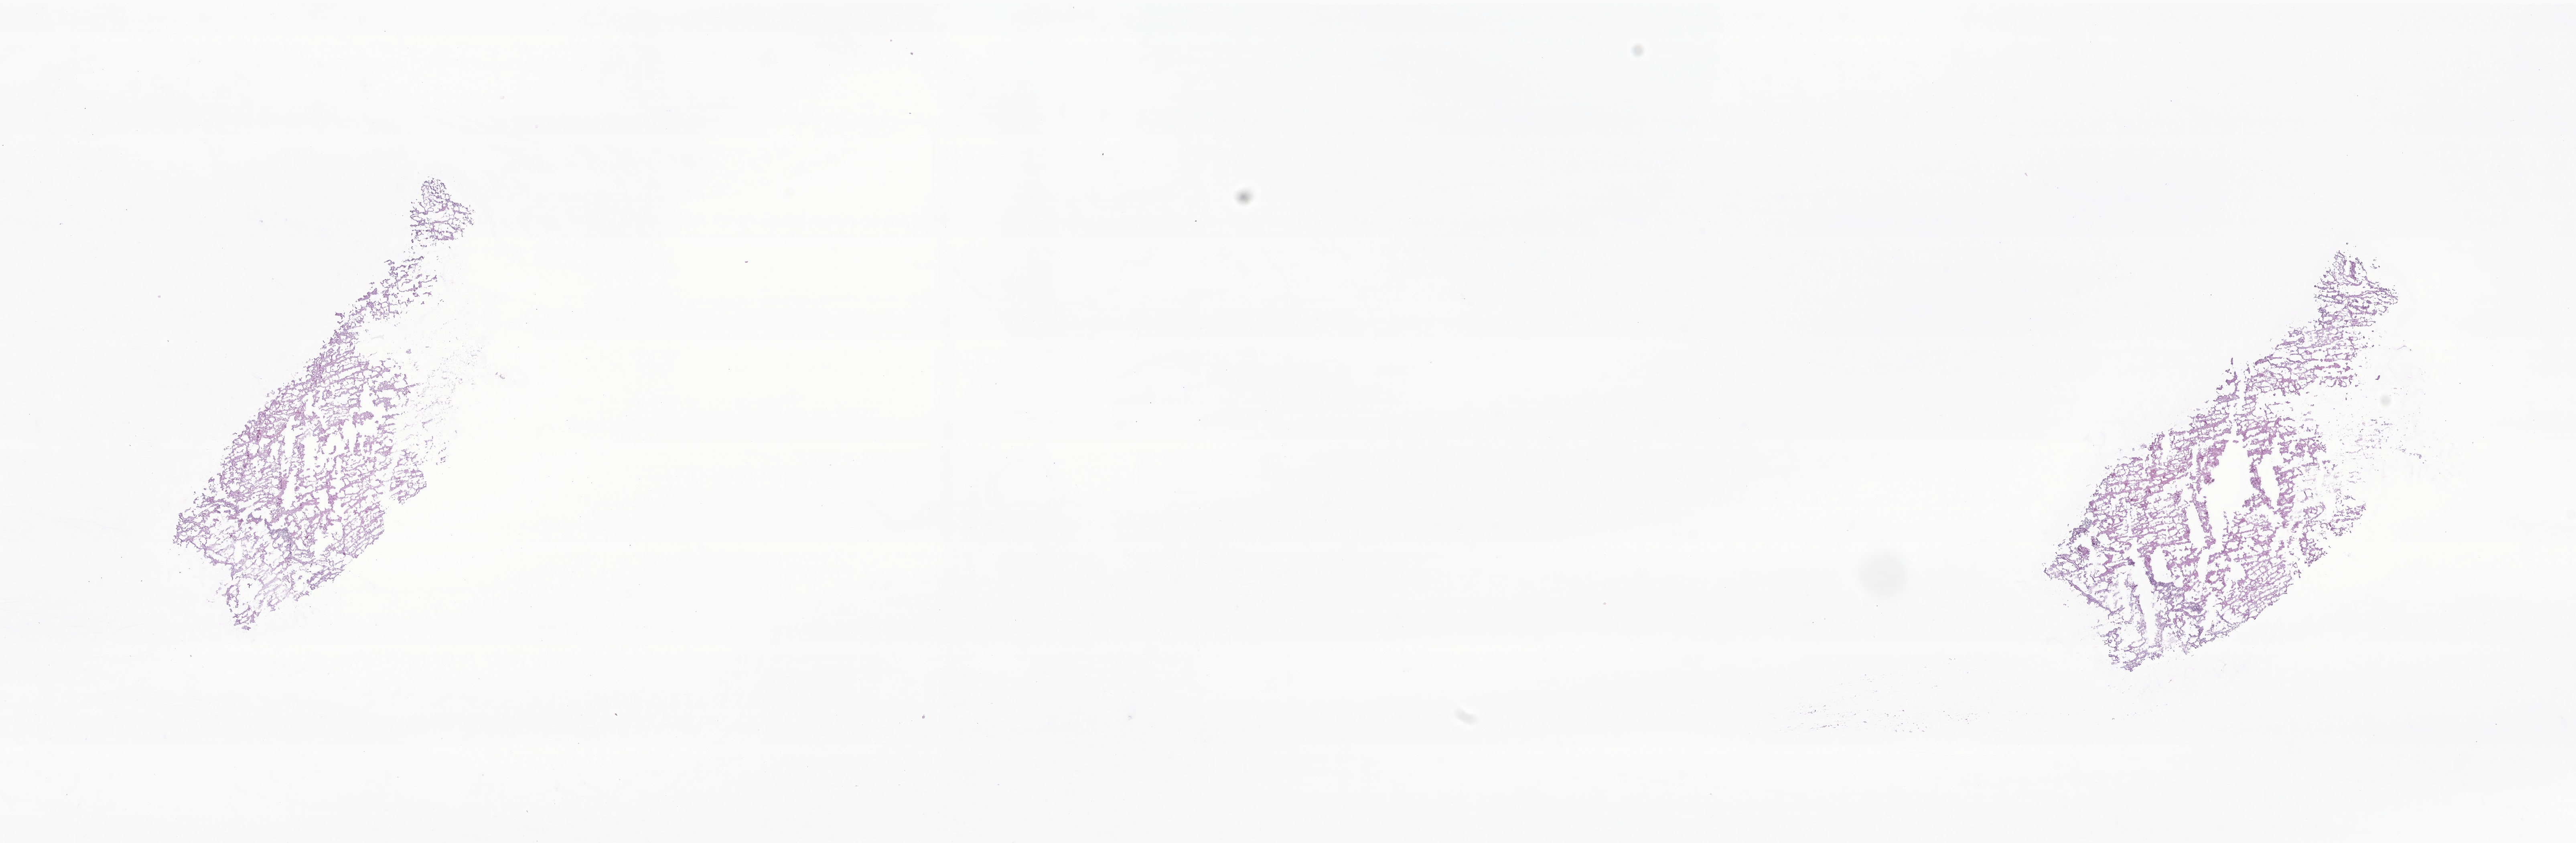
Digitized hematoxylin and eosin (H&E)-stained section of tumor tissue from the adrenal gland, shown as a low-resolution overview of the whole scanned area (about 27.1 x 8.9 mm); cryosection (OCT / tissue freezing medium). Patient: female, age 79 months (6 years 7 months).
* recorded diagnosis: Neuroblastoma, NOS